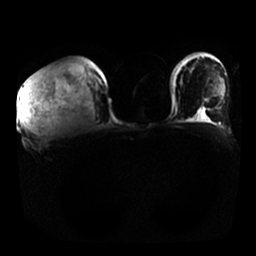
Breast MRI, one axial slice. Position 12 of 25 along the scan axis. Diffusion-weighted series; image 2 of 4 stored at this slice position (different b-values; order by instance number). 1.5 T. 4 mm slice thickness. 256 × 256 image matrix, field of view 350 × 350 mm. Female patient.
Outlined on this slice (expert manual segmentation):
- tumour on diffusion-weighted imaging: bounding box <20,72,53,136> (left, top, right, bottom; pixels)